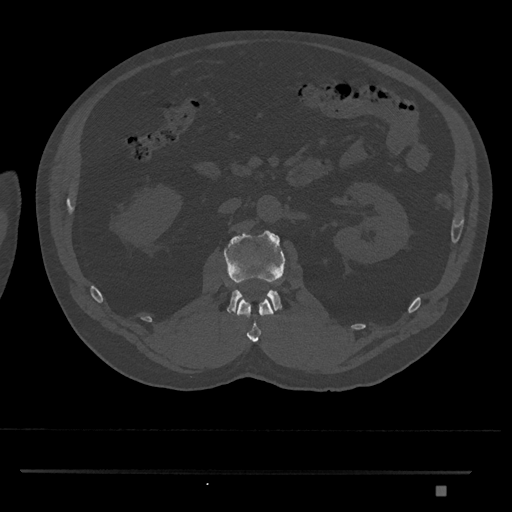
CT including the spine, one axial slice; position 784 of 1134 along the scan axis; bone window (W 1800 / L 400 HU); 0.5 mm slice thickness; 512 × 512 image matrix, field of view 429 × 429 mm. Patient: male, 65 years. Case-level facts recorded for this patient, not image findings: primary cancer: prostate.
Outlined on this slice (semi-automatic segmentation, software-assisted and operator-edited):
- L1 vertebra: bounding box <237,297,275,343> (left, top, right, bottom; pixels)
- L2 vertebra: <224,230,286,313>